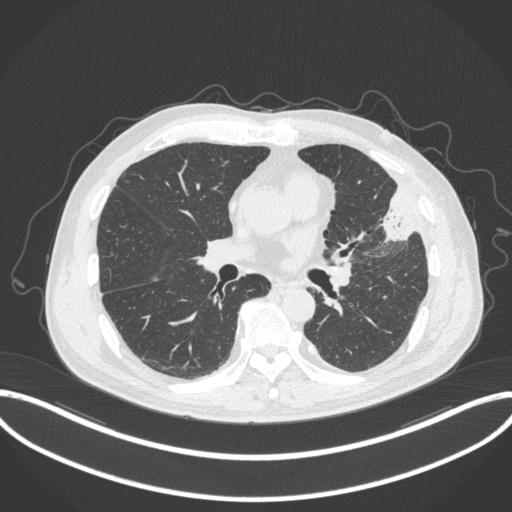
Chest CT, one axial slice. Position 173 of 382 along the scan axis. Reconstruction kernel B31f. Lung window (W 1500 / L -600 HU). 1 mm slice thickness. 512 × 512 image matrix, field of view 415 × 415 mm. Male patient, age 64 years. Case-level facts recorded for this patient, not image findings: clinical TNM (as recorded): T4 N1 M0; histopathological grade: G3.
Outlined on this slice (rectangle marked by the reading radiologist):
- lung tumour (recorded histology: adenocarcinoma): box from (x=378, y=185) to (x=415, y=243) px